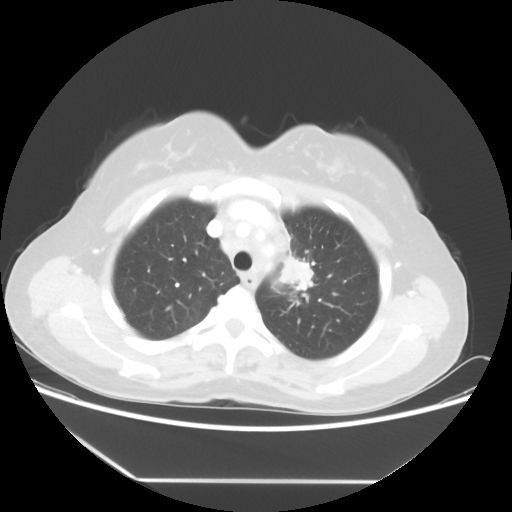
Chest CT, one axial slice; position 41 of 52 along the scan axis; reconstruction kernel STANDARD; 100 kVp; lung window (W 1500 / L -600 HU); 512 × 512 image matrix, field of view 390 × 390 mm. Female patient, age 50 years. From the clinical record (not read from this slice): clinical TNM (as recorded): T2 N3 M0.
Outlined on this slice (rectangle marked by the reading radiologist):
- lung tumour (recorded histology: adenocarcinoma): bounding box (x1, y1, x2, y2) in pixels: (271, 248, 315, 295)